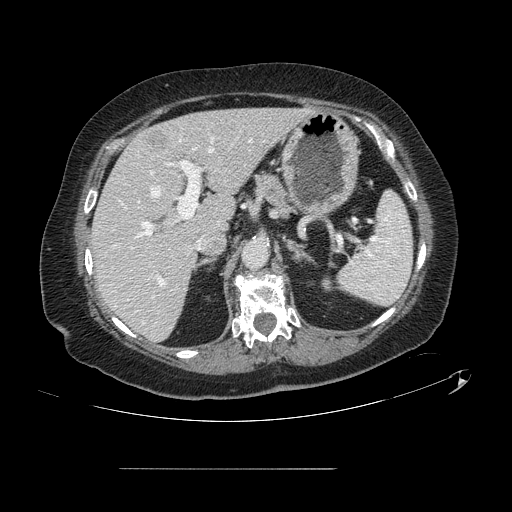
Contrast-enhanced abdominal CT, one axial slice; position 80 of 148 along the scan axis; soft-tissue window (W 400 / L 40 HU); 512 × 512 image matrix, field of view 439 × 439 mm. Female patient, age 75 years. Case-level facts recorded for this patient, not image findings: diagnosis: colorectal cancer liver metastases, imaged before liver resection; multiple liver metastases: no.
Annotated regions visible in this slice (manually delineated by an expert):
- hepatic veins: bounding box (x1, y1, x2, y2) in pixels: (152, 149, 213, 197)
- liver: (92, 108, 305, 341)
- planned liver remnant (the part of the liver to remain after resection): (92, 108, 304, 341)
- portal vein (with intrahepatic branches): (134, 138, 265, 286)
- liver metastasis: (146, 130, 169, 152)